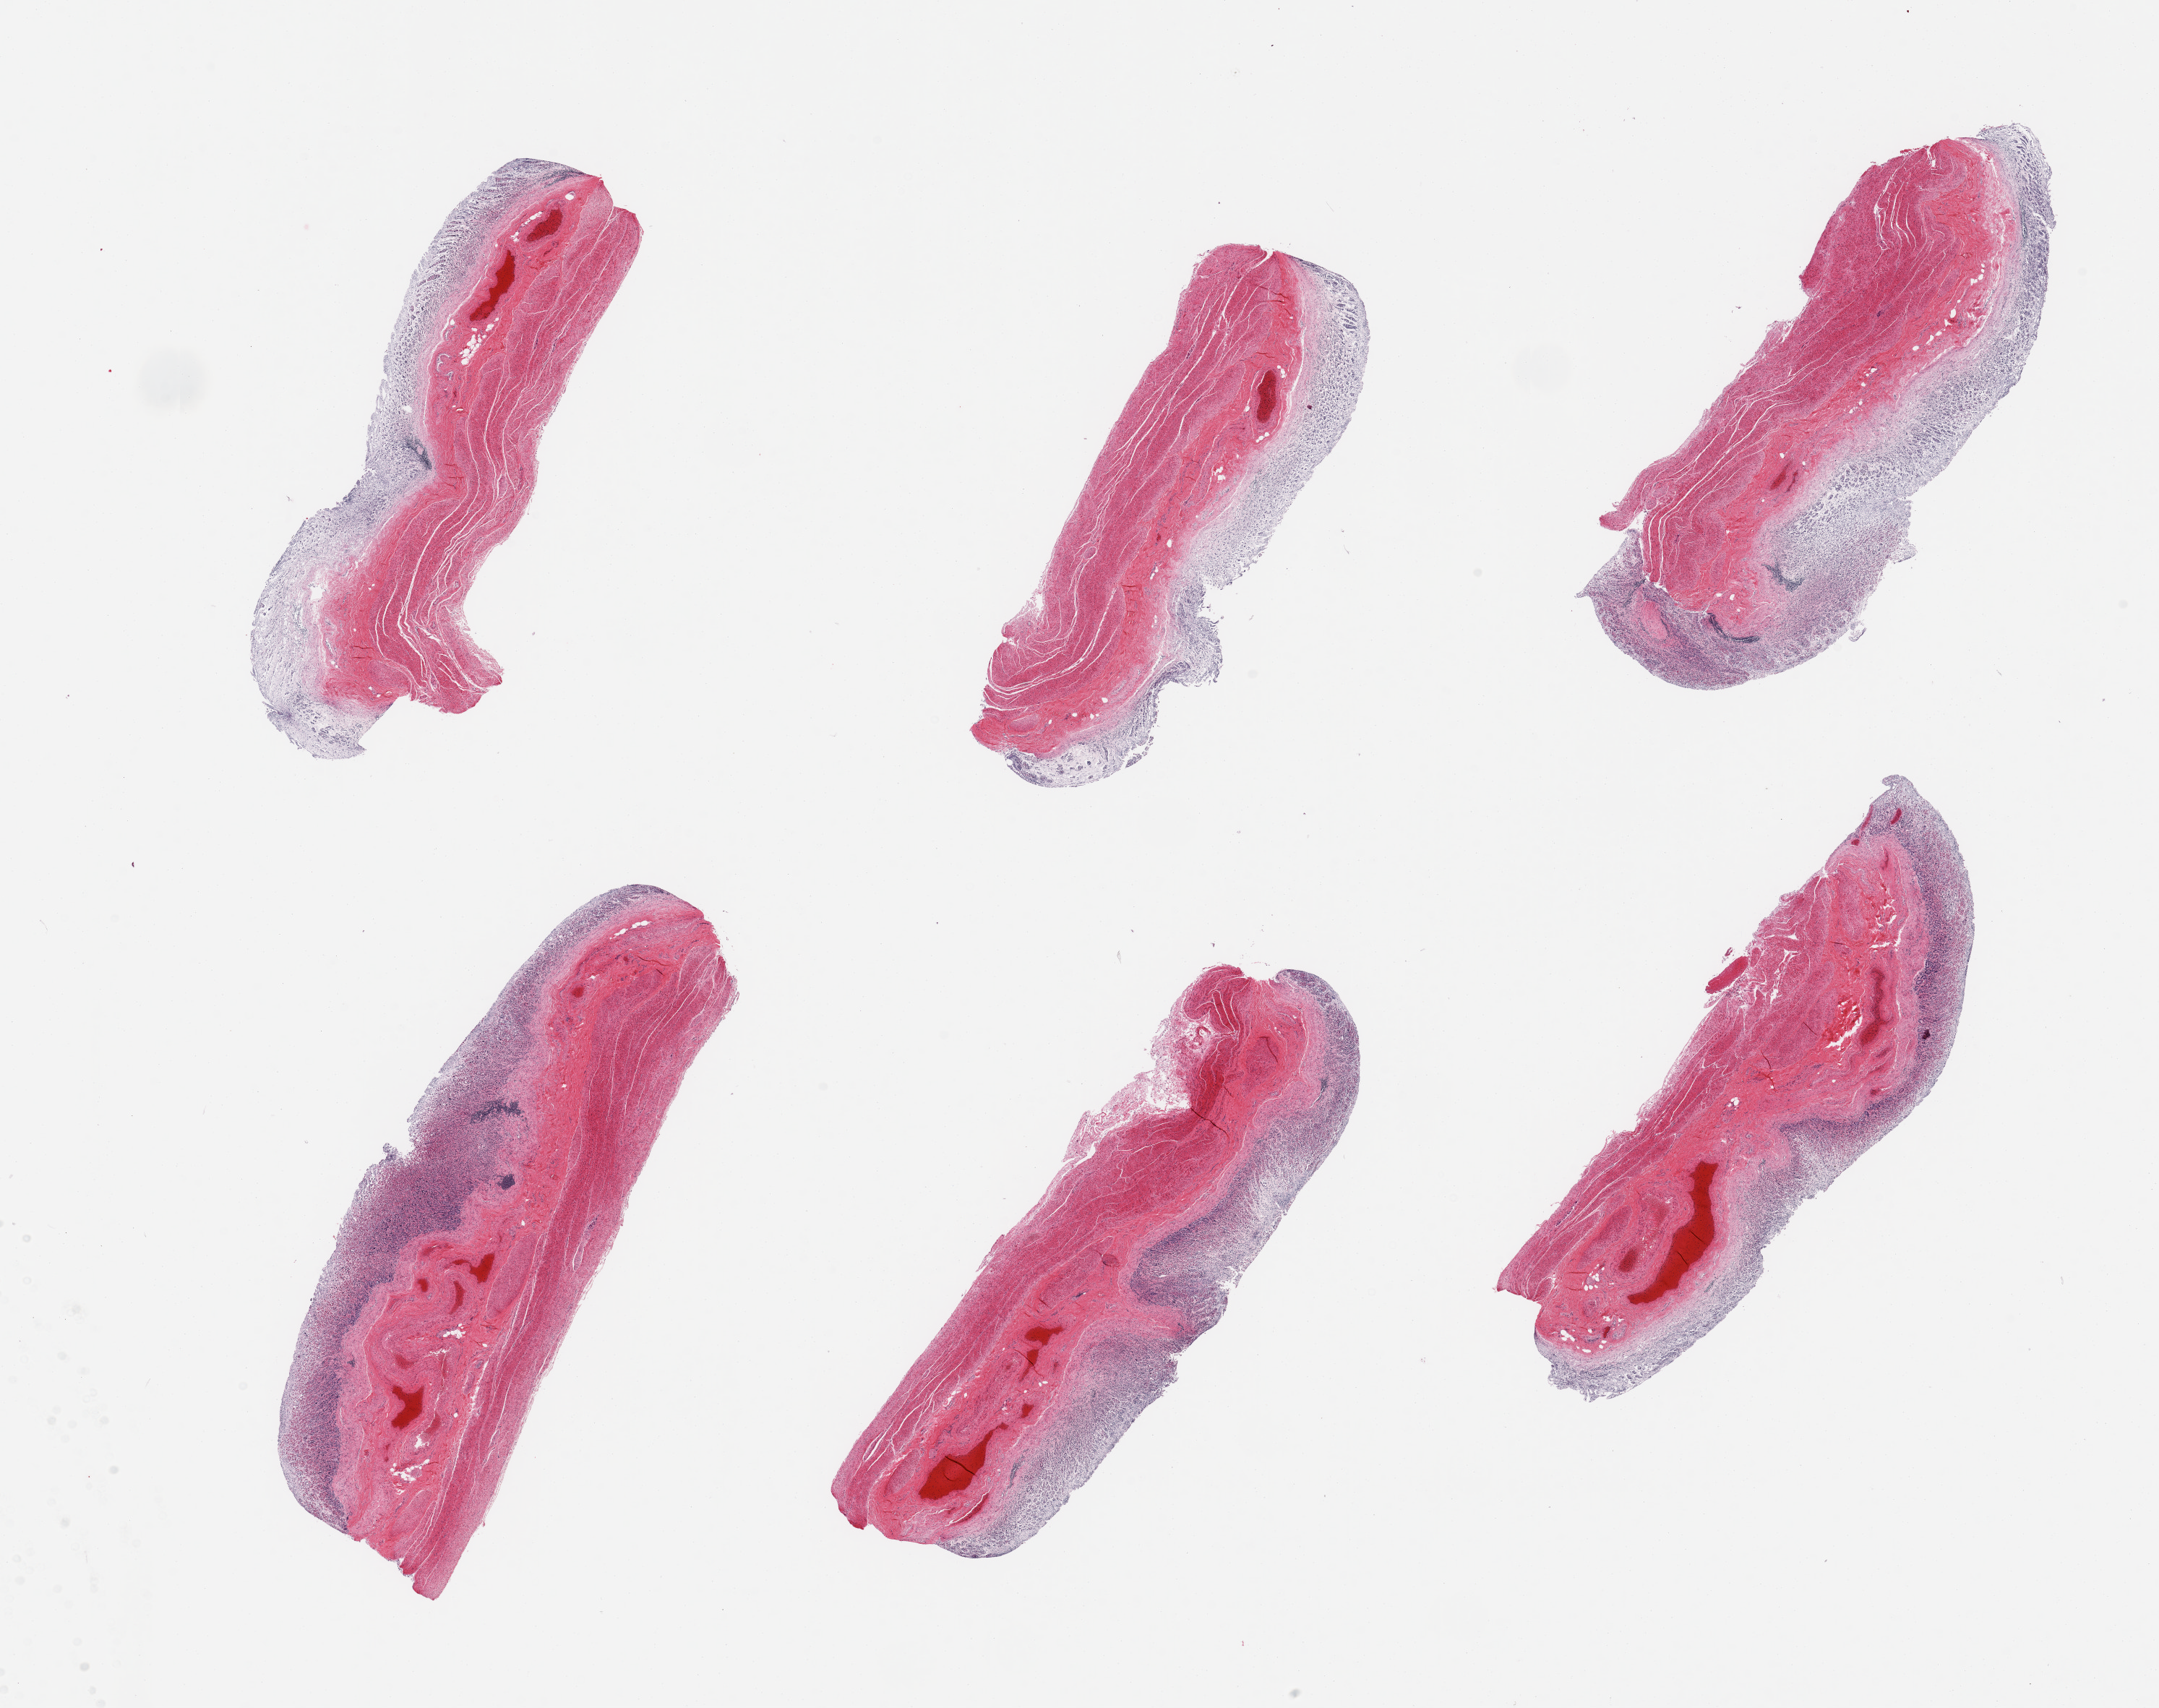
Whole-slide image, H&E stain, brightfield — shown as a low-resolution overview of the whole scanned area (about 23.6 x 18.7 mm). PAXgene-fixed paraffin-embedded (PFPE) section. Section of stomach (target tissue). Tissue donor sample.
Reviewer comment on this tissue sample: 6 pieces; severely autolyzed mucosa, moderately autolyzed muscularis, congestion.